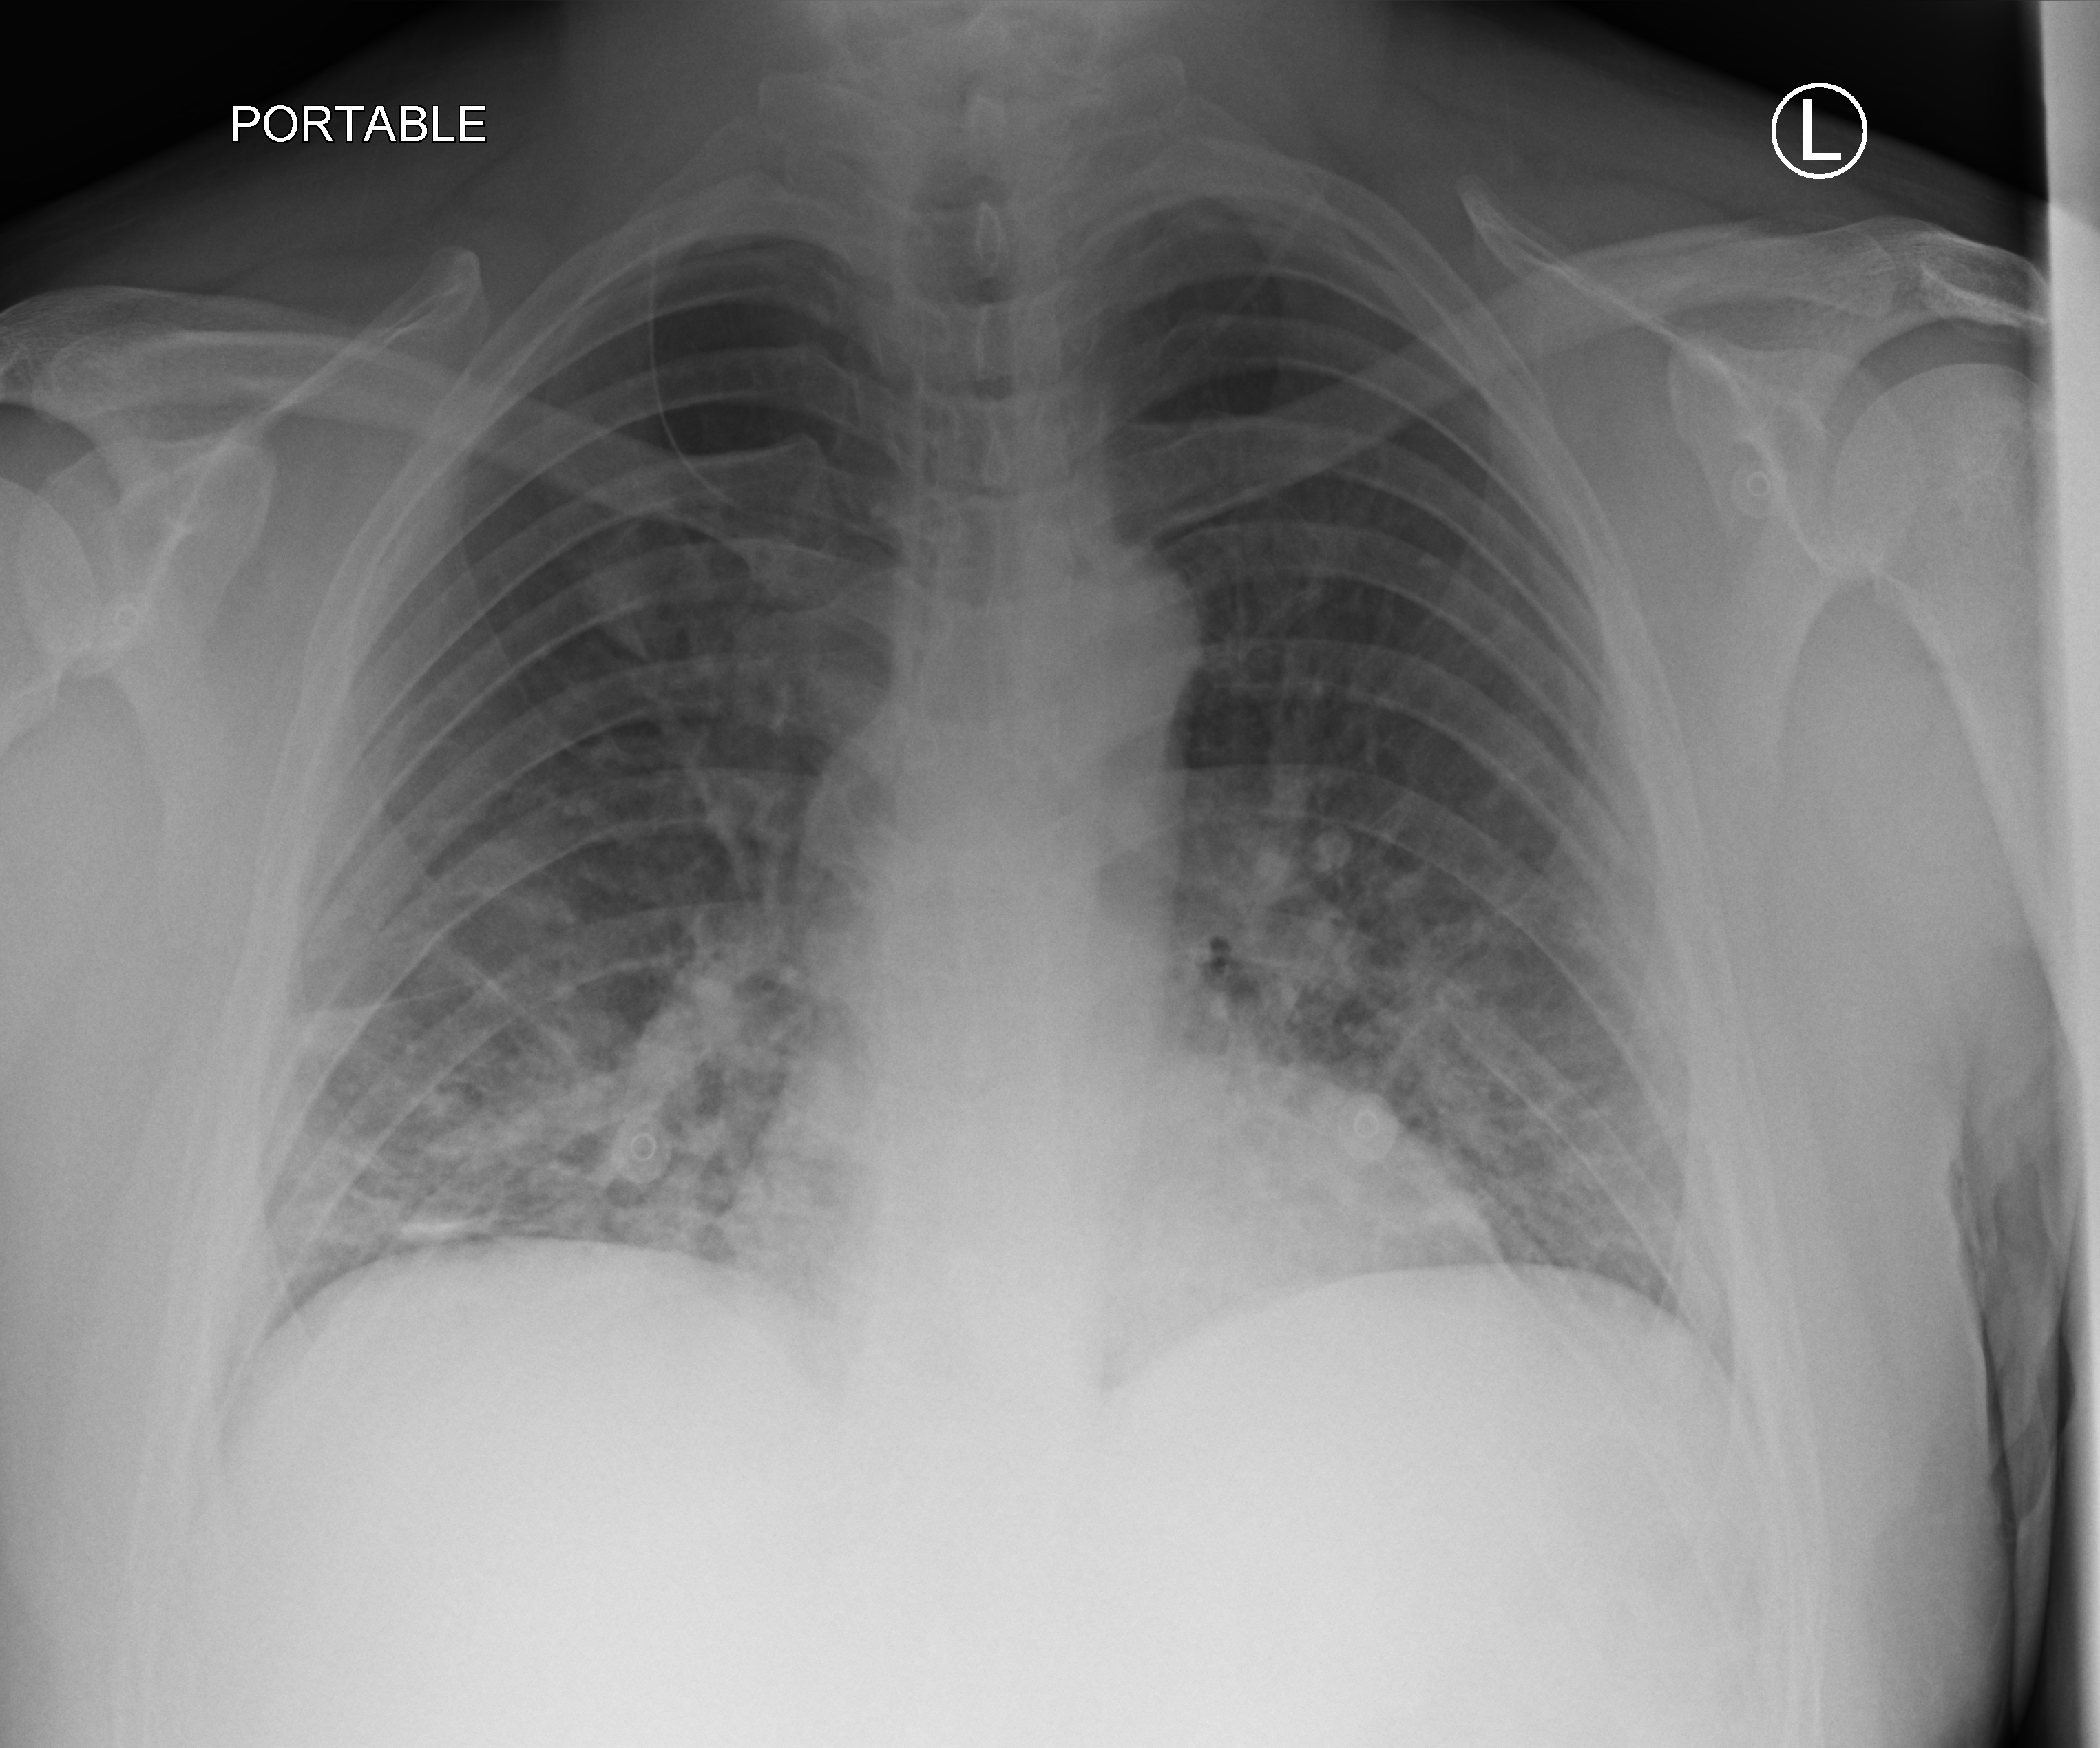
Chest X-ray (portable); anteroposterior (AP) projection. Male patient hospitalised with COVID-19, age 18–59 years.
Hospital-stay facts (about this admission, not read from this image; timing relative to this image not recorded):
- smoking status (admission record): never
- admitted to intensive care during this hospital stay: no